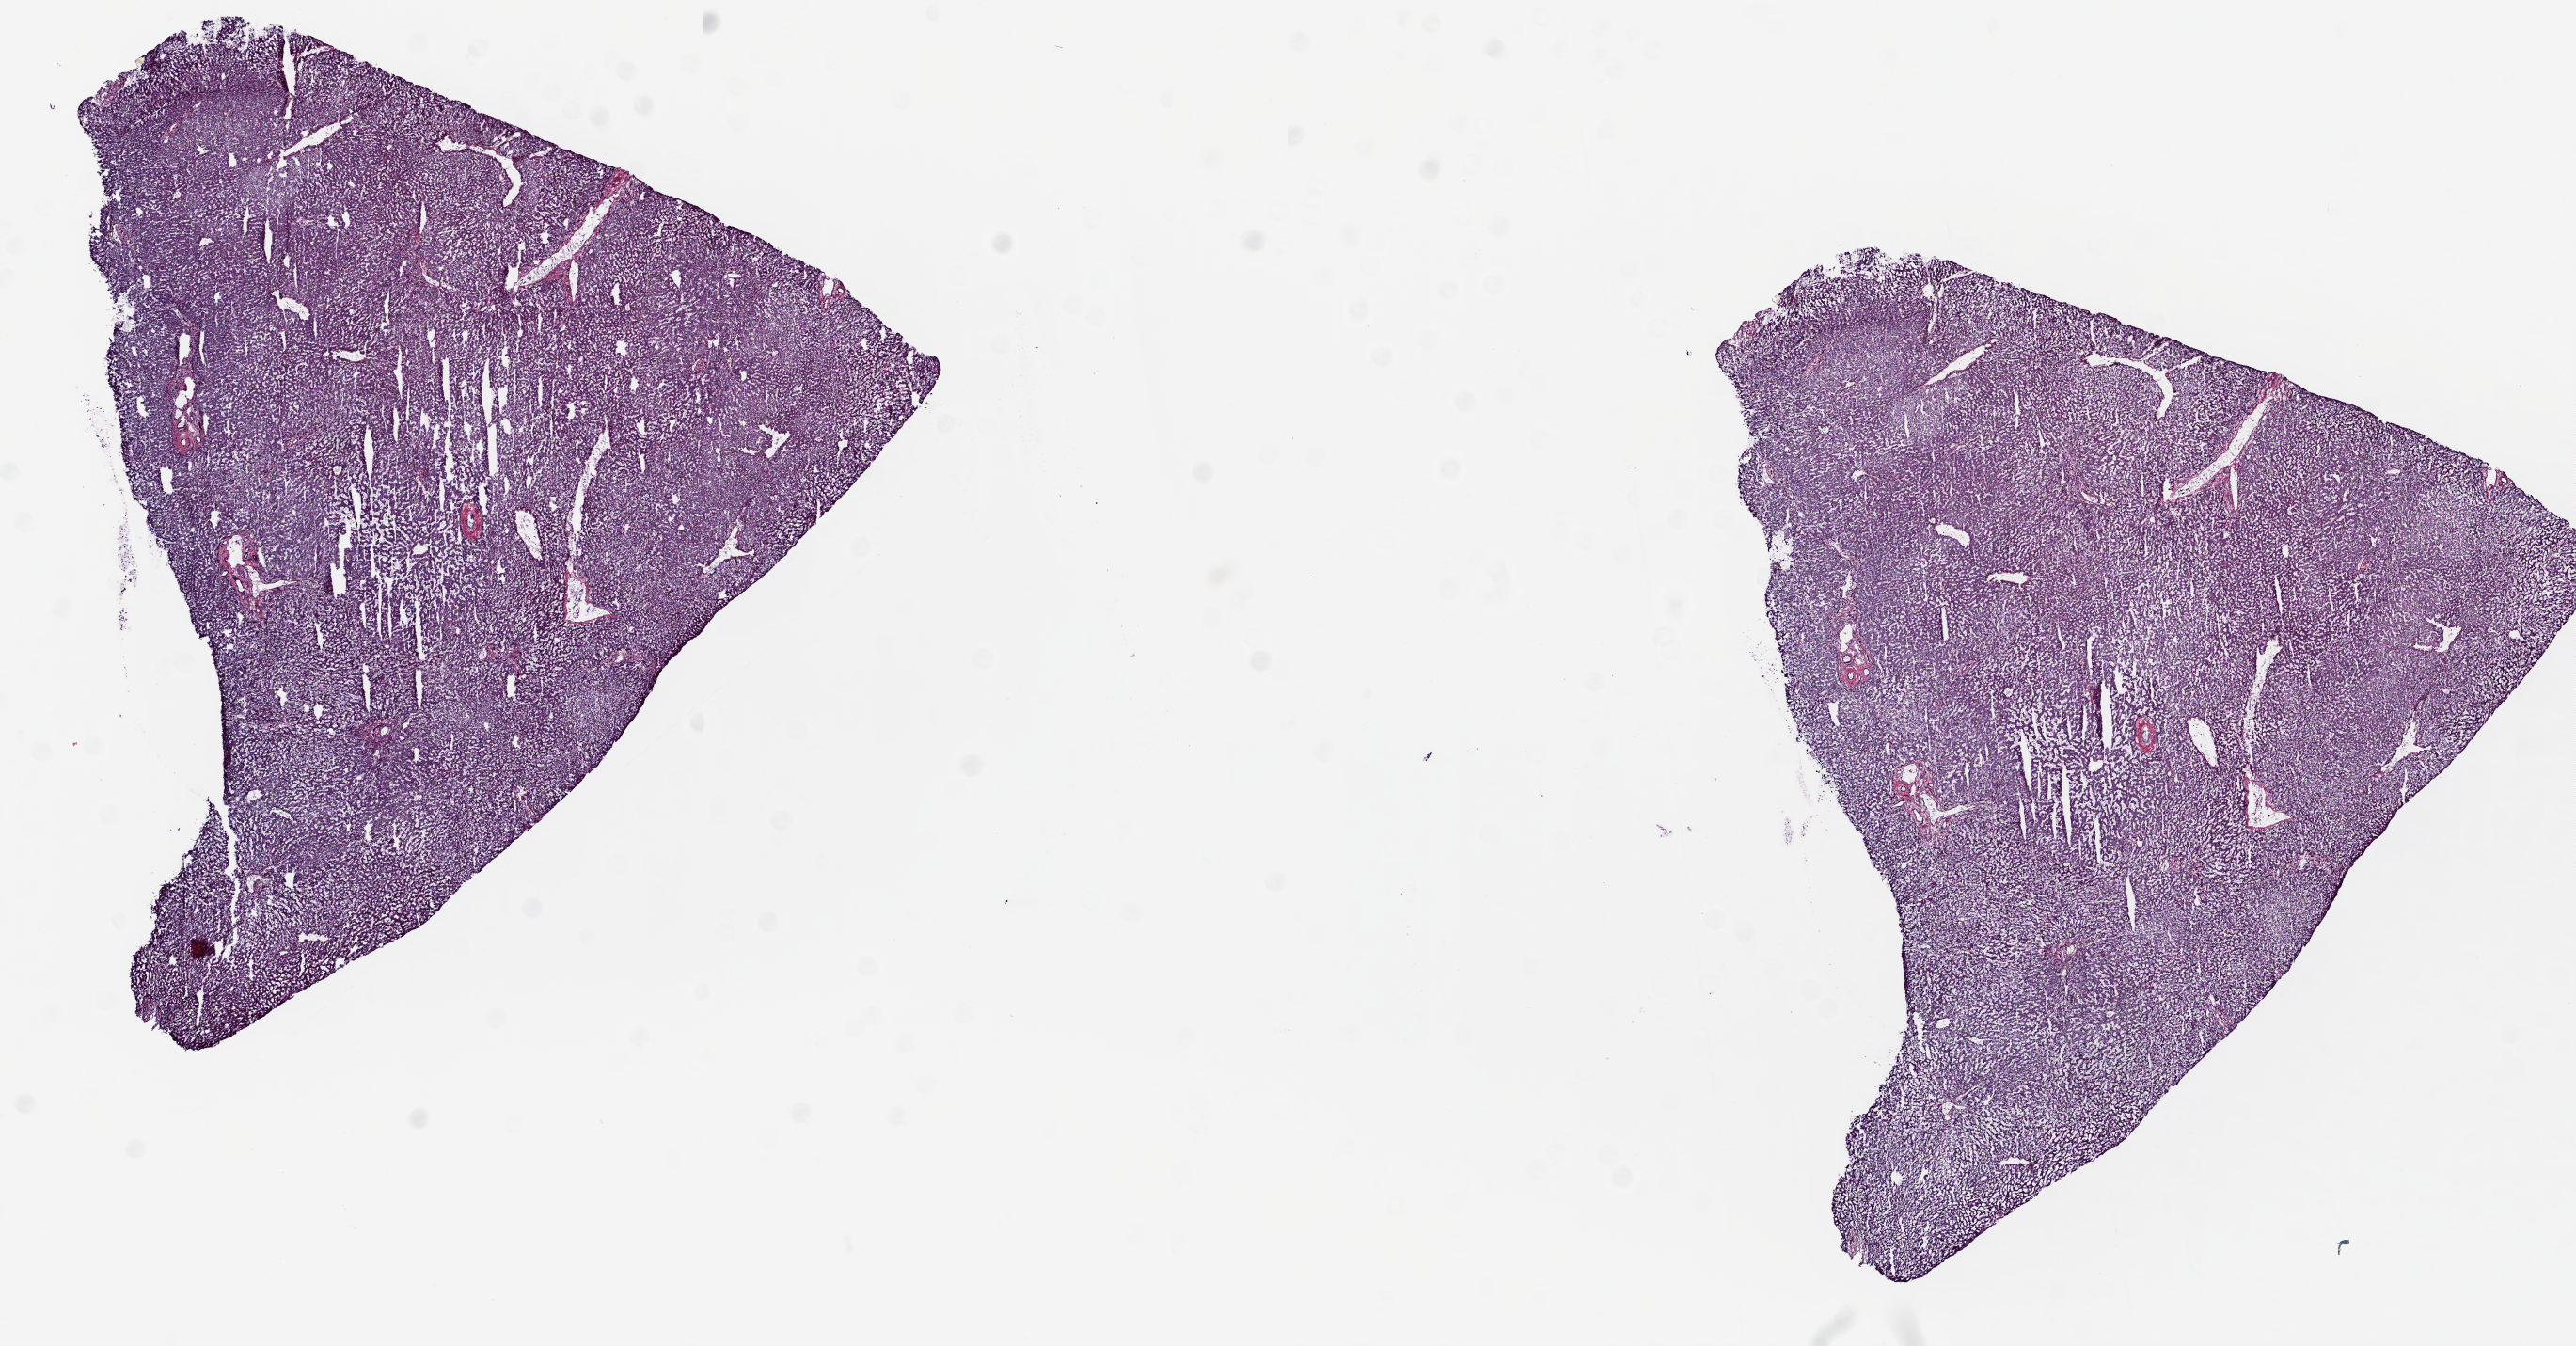
Hematoxylin and eosin (H&E) stained whole-slide image — low-resolution overview of the scanned area, about 21.8 x 11.4 mm (slide scanned at 20x). Frozen section from the top of the tissue portion. Liver, solid tissue normal (non-tumour tissue) sample. Female, age 51 years at initial diagnosis. Pathologist review of this section (percent, as recorded): tumour cells 0%, tumour nuclei 0%.
This section: solid tissue normal sample (biorepository sample class). Patient diagnosis: Hepatocellular carcinoma, NOS.